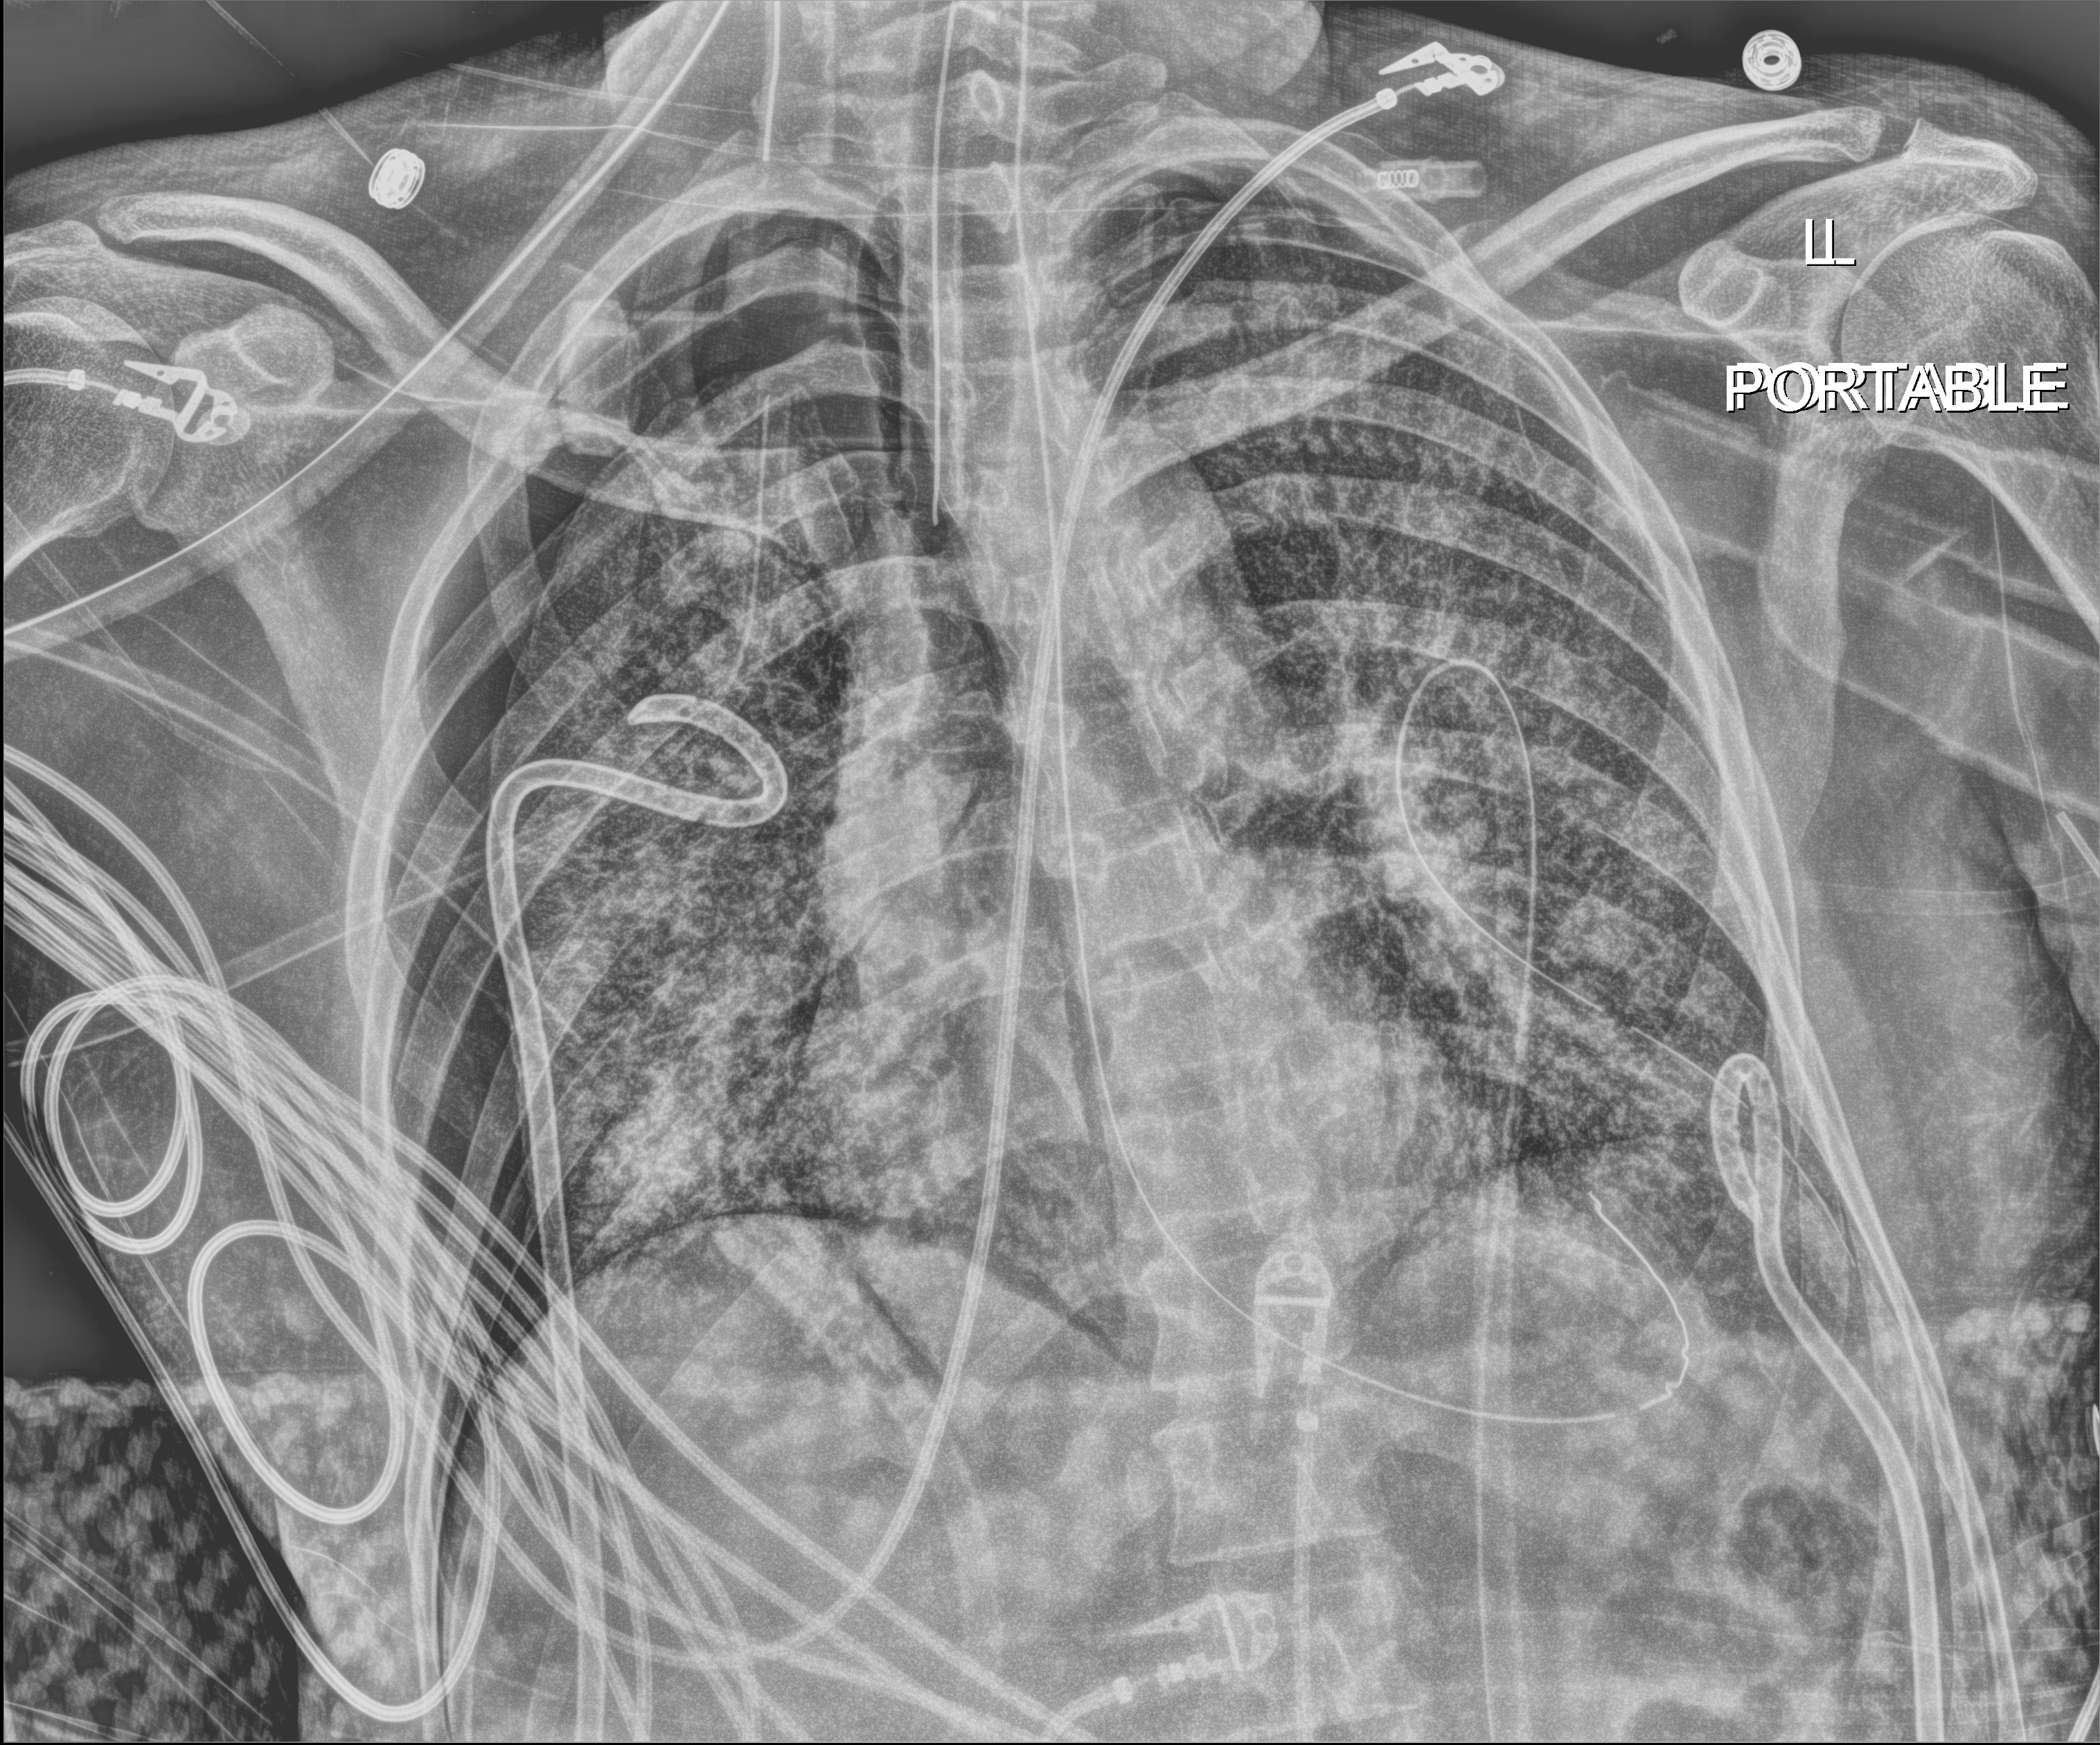
Chest X-ray (portable). Adult patient hospitalised with COVID-19, age 18–59 years.
Admission-level facts for this patient (not findings on this image; timing relative to this image not recorded):
- mechanically ventilated during this hospital stay: yes
- admitted to intensive care during this hospital stay: yes
- hypertension (admission record): no